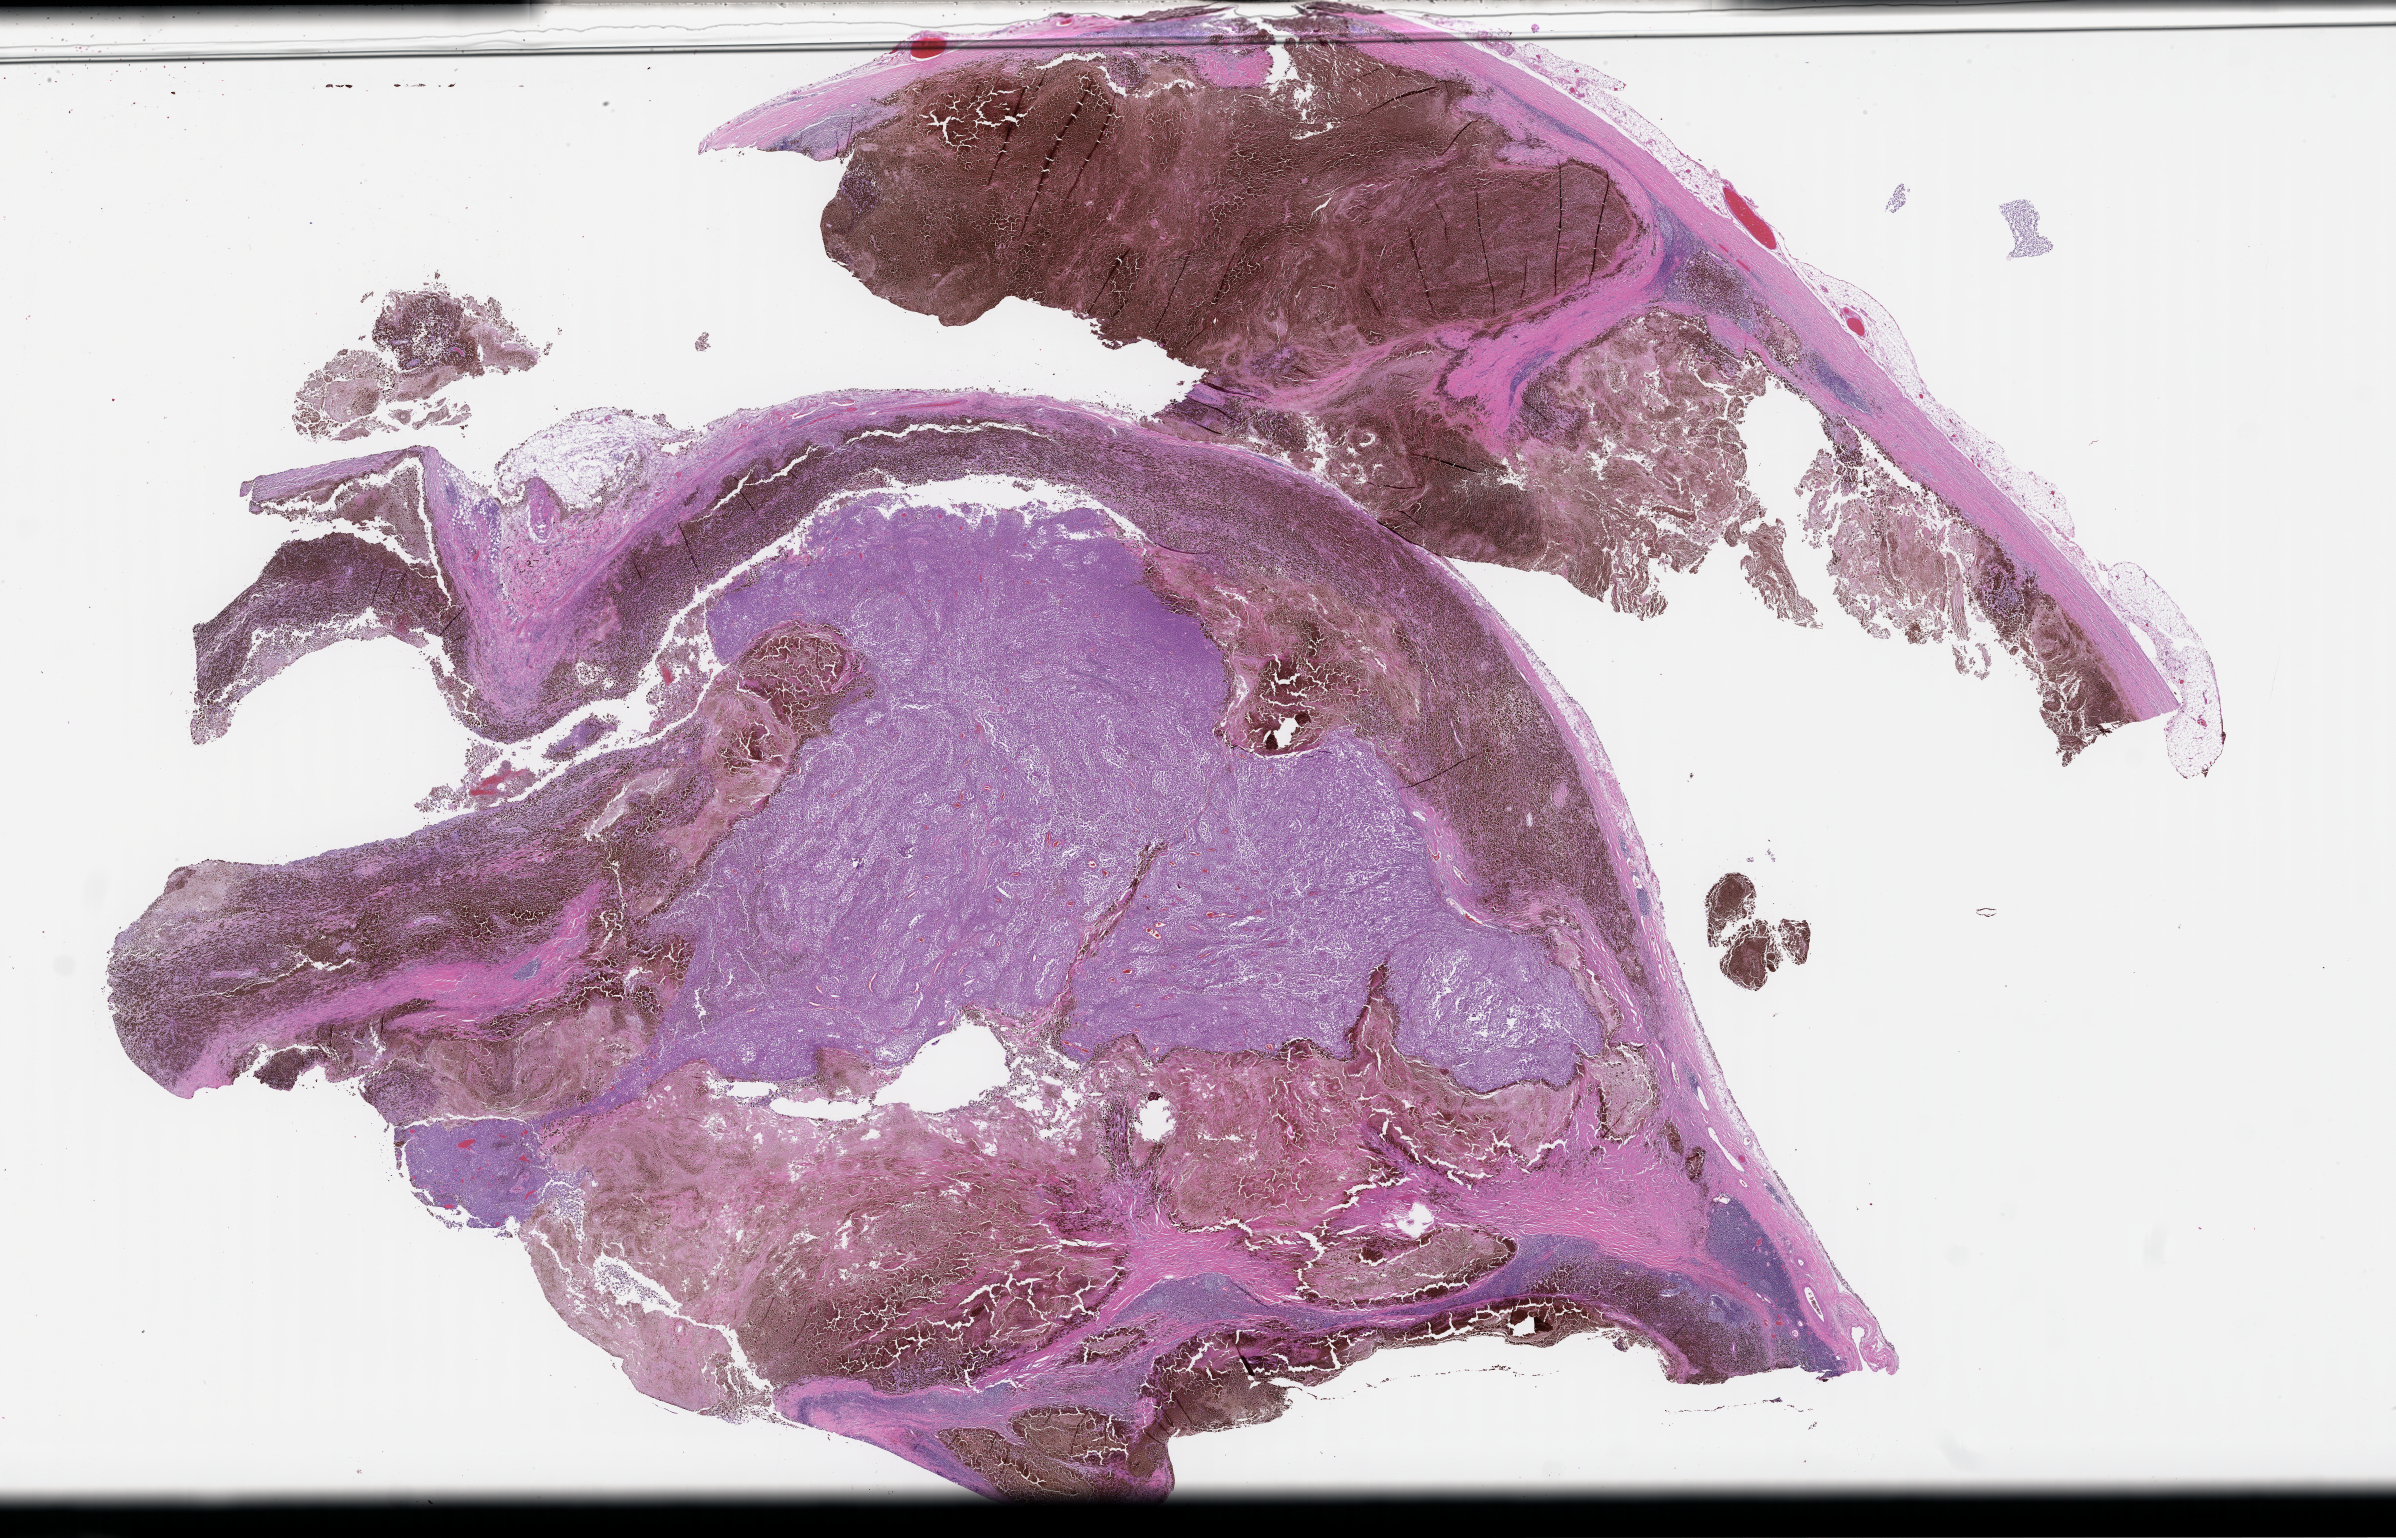
Whole-slide image, haematoxylin and eosin stain — shown as a low-resolution overview of the whole scanned area (about 38.7 x 24.8 mm); formalin-fixed paraffin-embedded section; site: skin; specimen time point: archival tissue. Patient sex: male.
This section: primary tumor. Diagnosis: Melanoma.